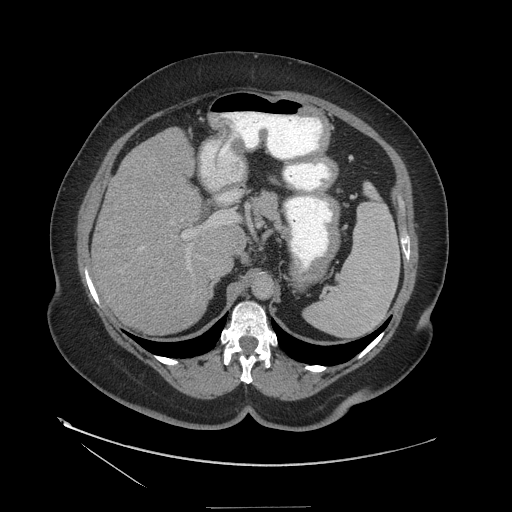
Contrast-enhanced abdominal CT (liver protocol), one axial slice. Position 75 of 127 along the scan axis. Reconstruction kernel STANDARD. Soft-tissue window (W 400 / L 40 HU). 2.5 mm slice thickness. 512 × 512 image matrix, field of view 480 × 480 mm. Case-level facts recorded for this patient, not image findings: diagnosis: hepatocellular carcinoma (patient treated with transarterial chemoembolisation; whether this scan precedes or follows treatment is not stated here); TNM stage (as recorded): Stage-II; Child-Pugh class: A; tumour differentiation: well differentiated; tumour nodularity: multinodular.
Outlined on this slice (semi-automatically segmented with operator editing):
- liver parenchyma outside the tumour (the mass and vessels are separate outlines, so this box may not span the whole liver): bounding box (x1, y1, x2, y2) in pixels: (92, 128, 245, 334)
- liver vessels: (182, 213, 236, 250)